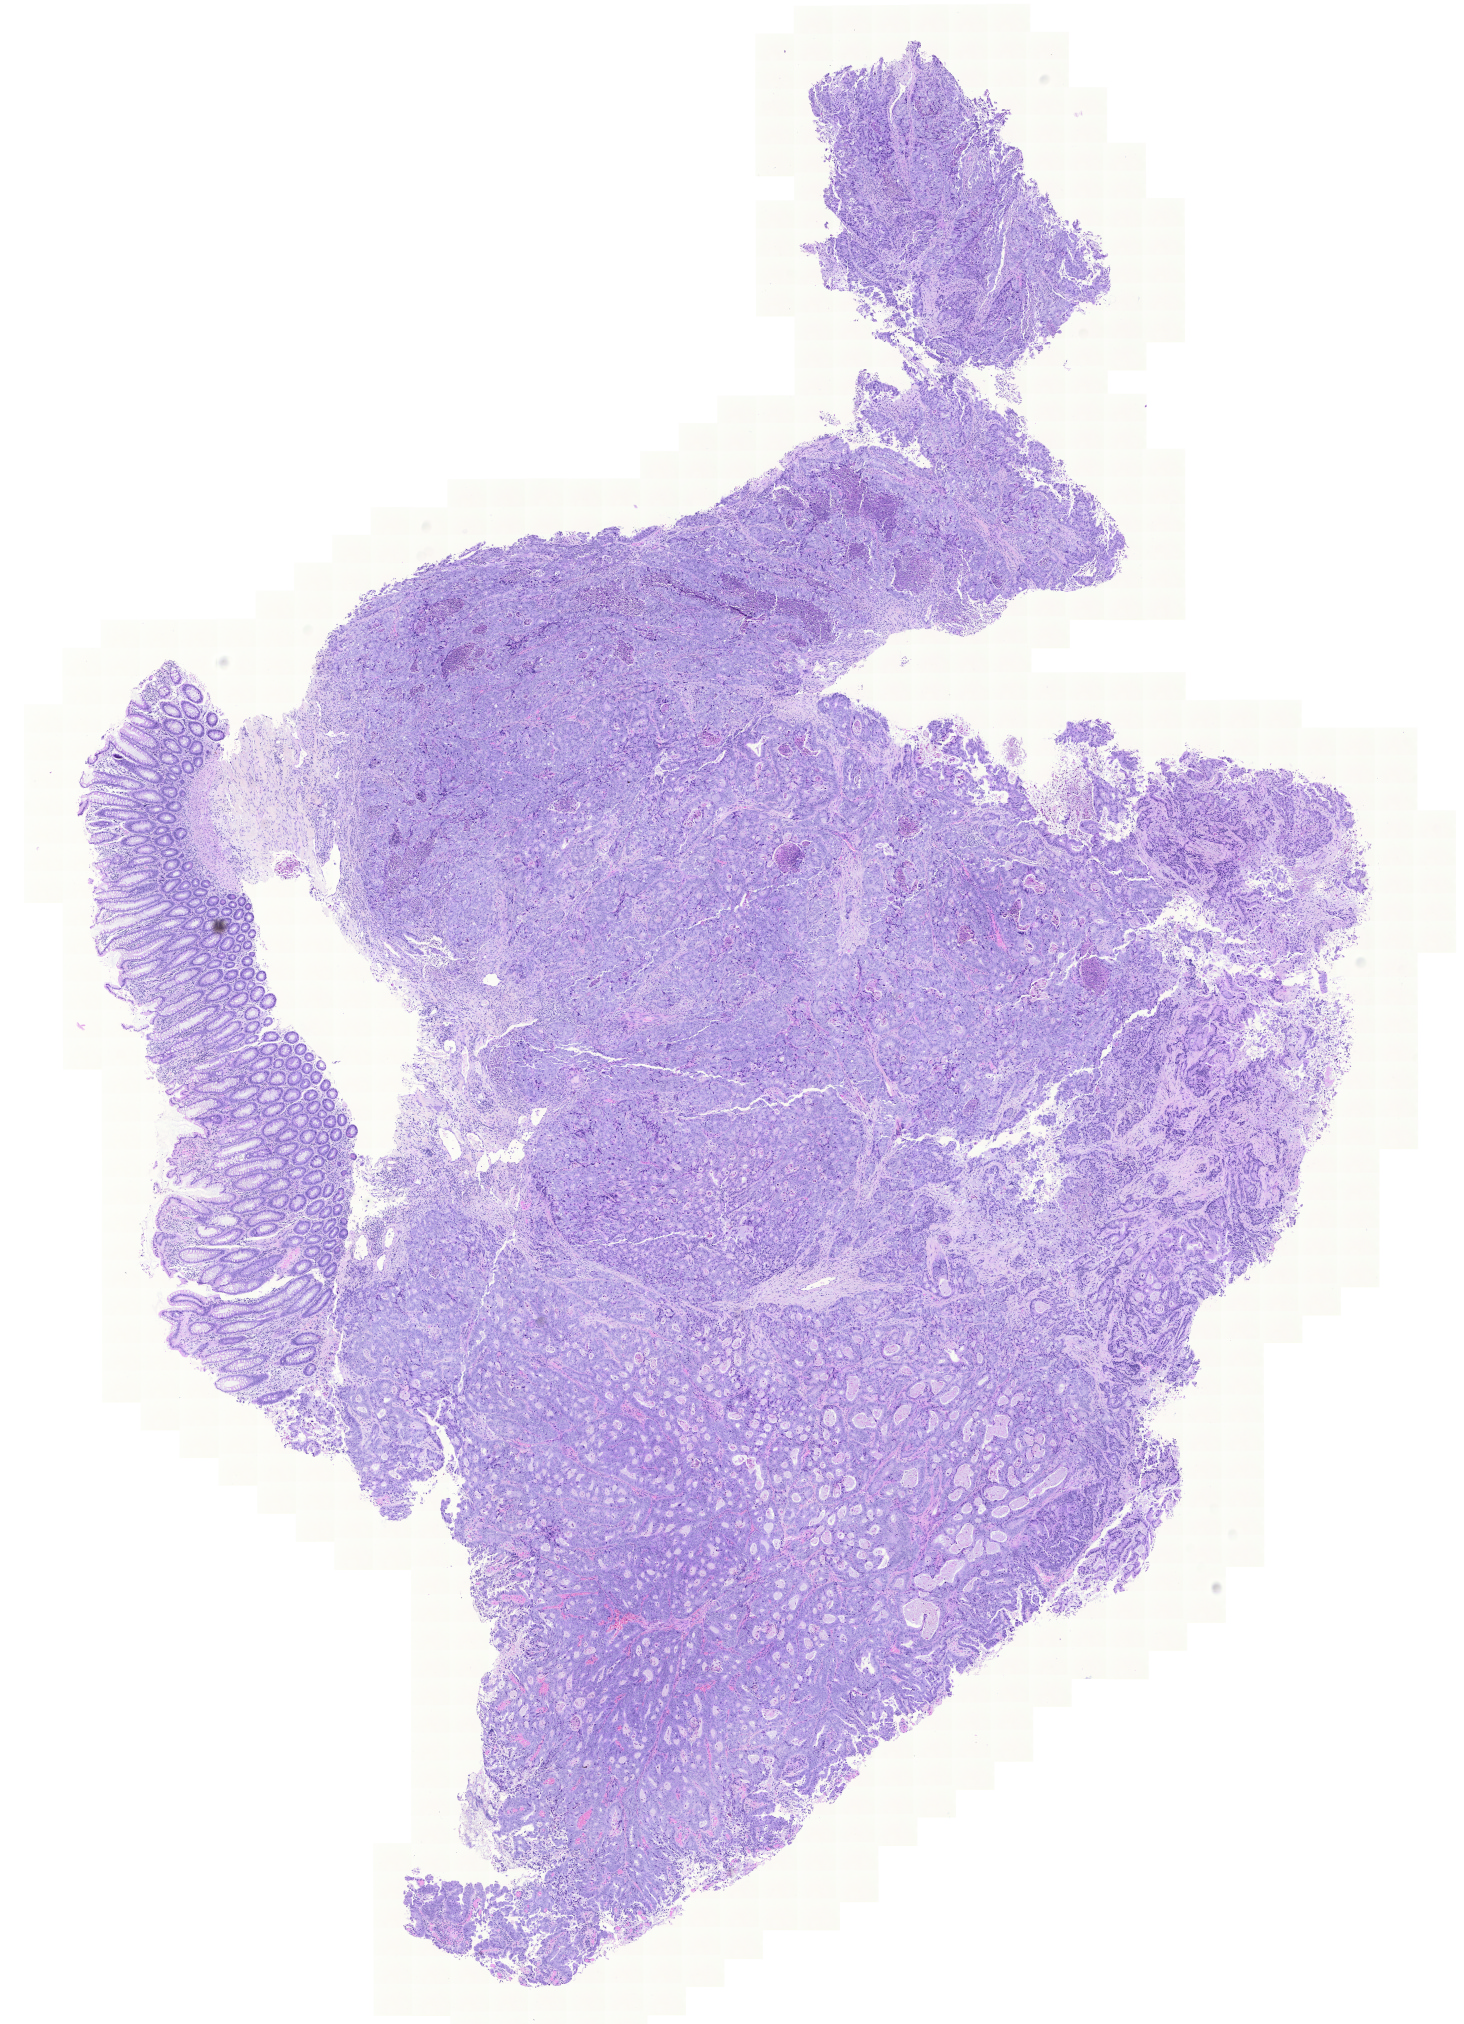
Hematoxylin and eosin (H&E) stained whole-slide image, whole scanned area (about 10.9 x 15.1 mm, from a 20x scan) shown as a low-resolution overview, formalin-fixed paraffin-embedded (FFPE) diagnostic section, colon, primary tumour sample. Patient: male, age at initial diagnosis 50 years.
* TNM: T4 N2 M1
* AJCC pathologic stage: IV
* pathologic diagnosis: Adenocarcinoma, NOS (ascending colon)